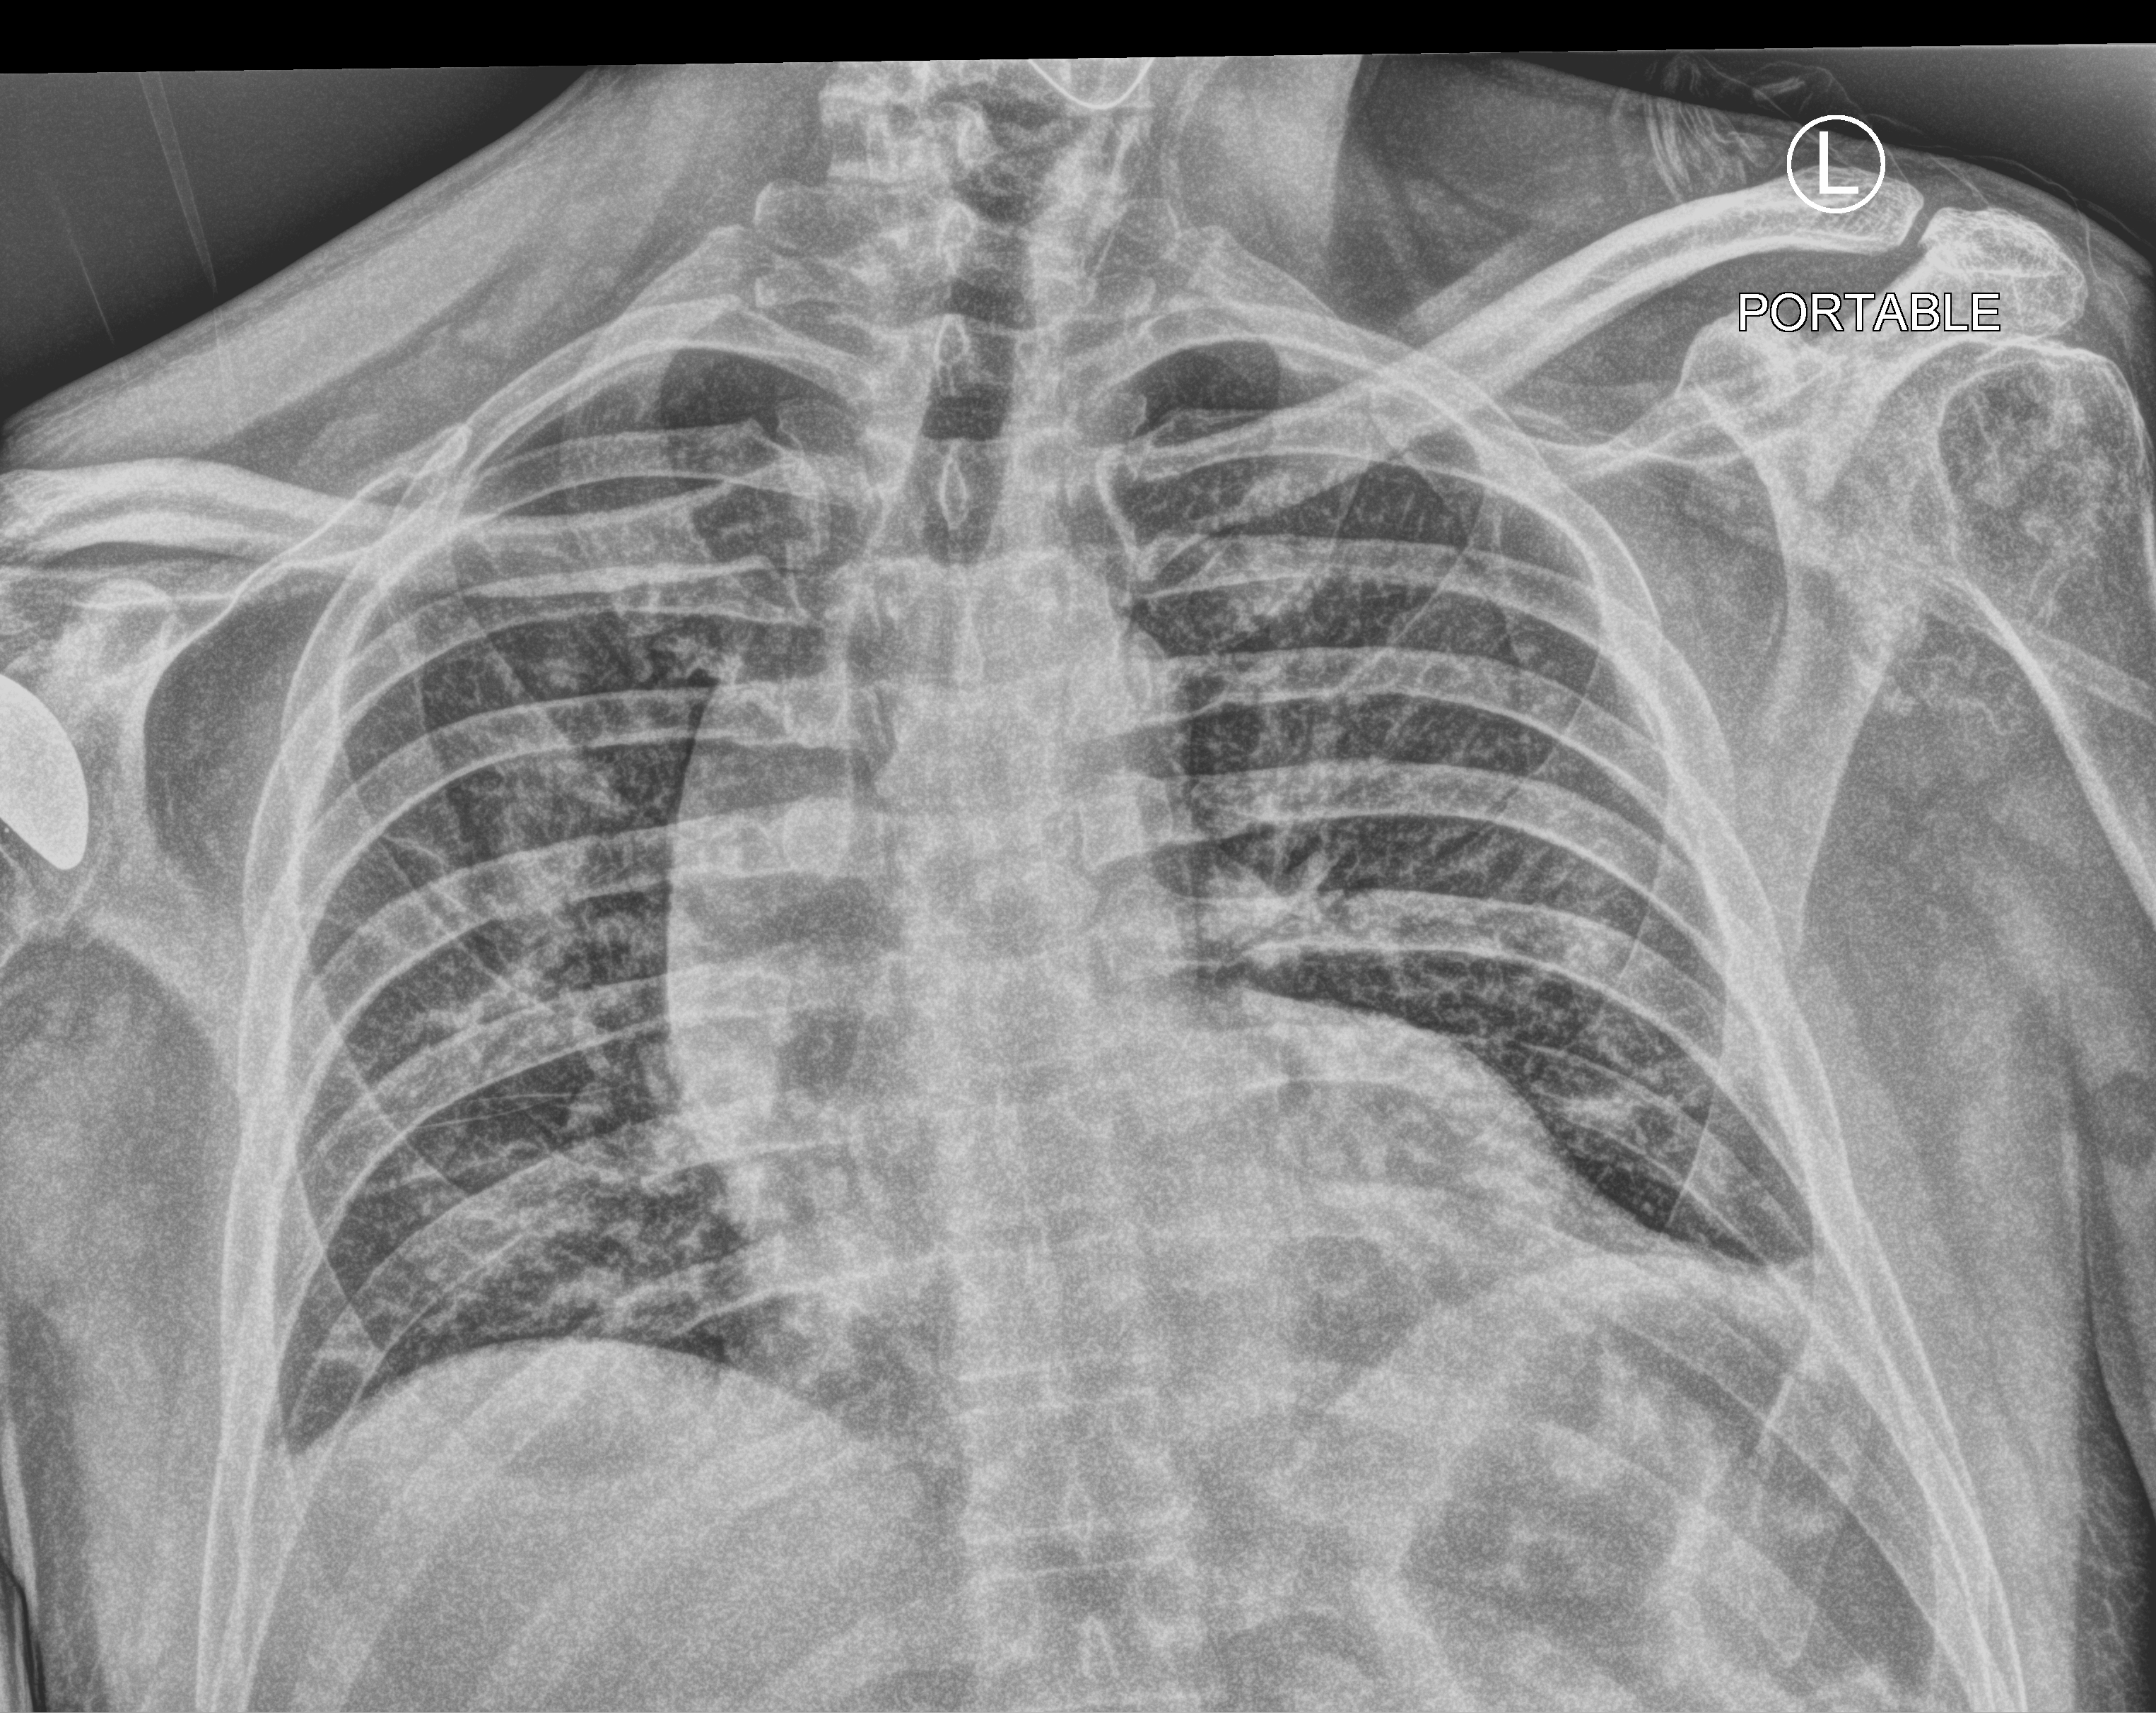
Bedside chest radiograph (computed radiography), anteroposterior (AP) projection. Male patient hospitalised with COVID-19, age 60–74 years.
Admission-level facts for this patient (not findings on this image; timing relative to this image not recorded): admitted to intensive care during this hospital stay: no.